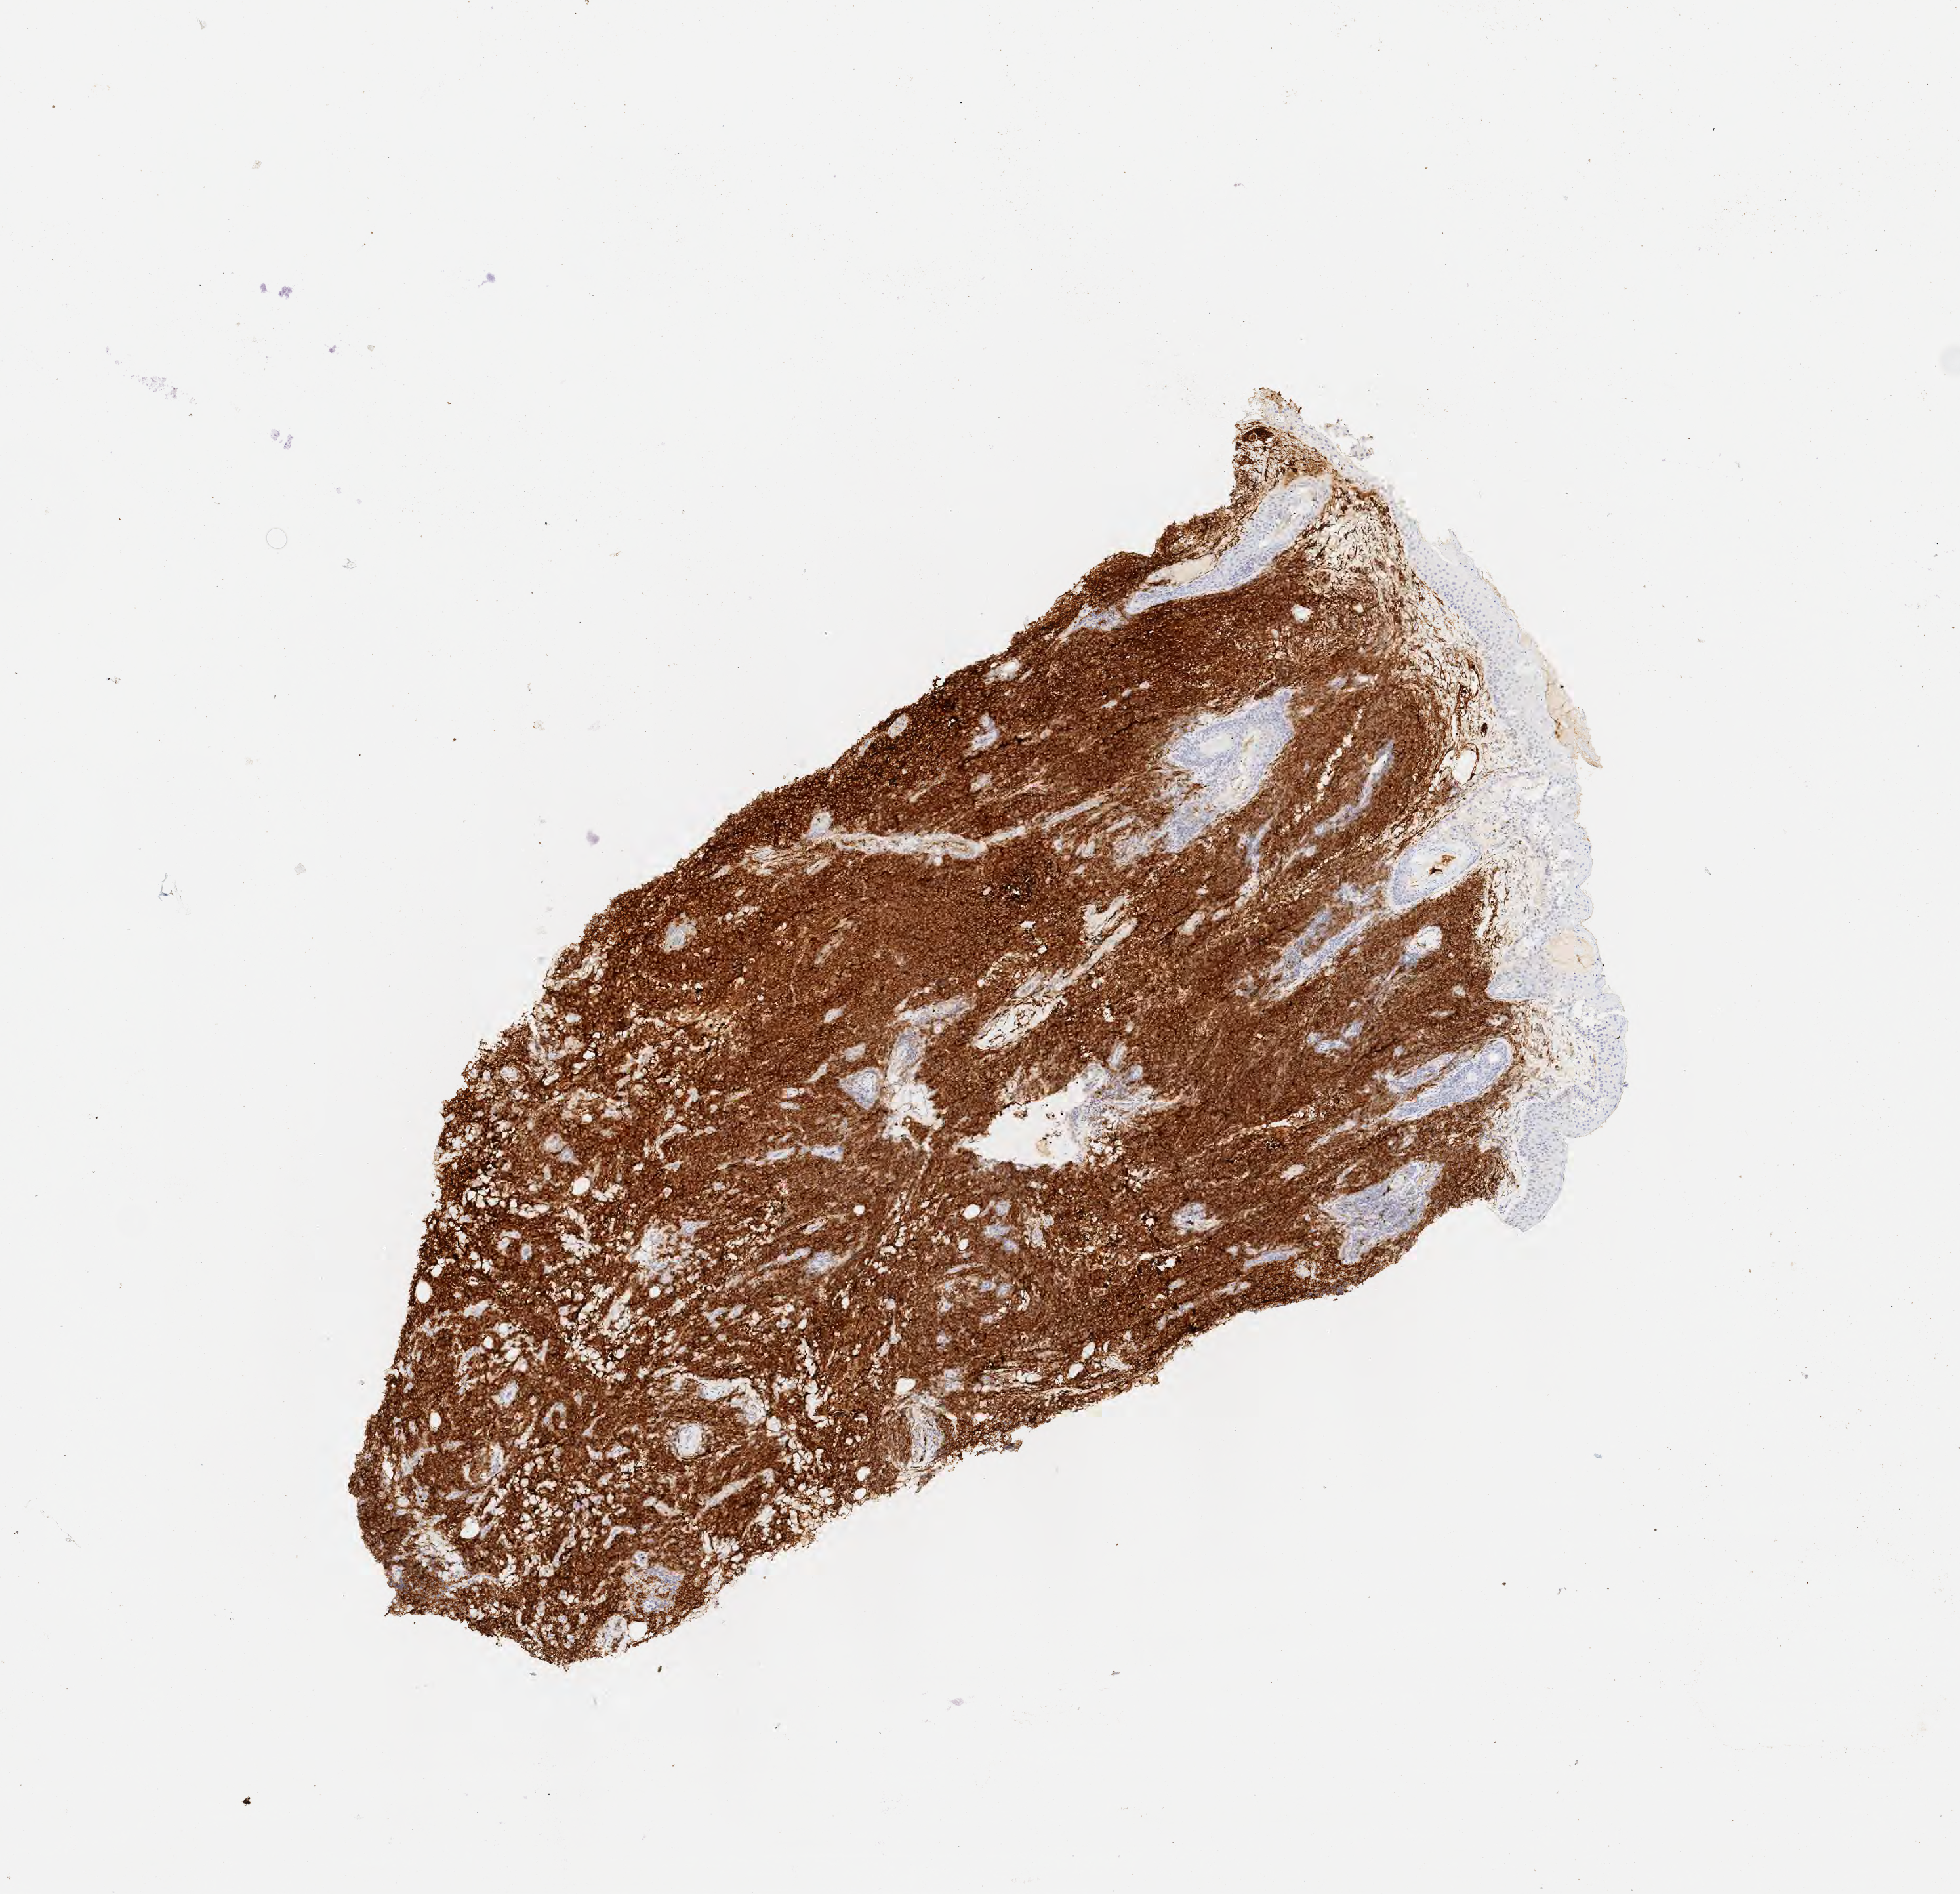
Immunohistochemistry (IHC) whole-slide image stained for CD10, whole scanned area (about 6.0 x 5.8 mm) shown as a low-resolution overview. Tumor tissue. Patient: male, 41 years old.
Diagnosis: Diffuse large B-cell lymphoma, NOS.